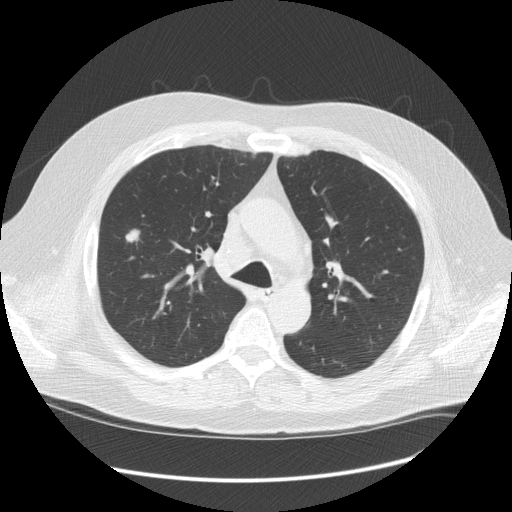
Low-dose screening chest CT, one axial slice; slice 89 of 128 in the series (ordered by position); reconstruction kernel STANDARD; lung window (W 1500 / L -600 HU); 2.5 mm slice thickness; 512 × 512 image matrix, field of view 401 × 401 mm.
Outlined on this slice (expert manual segmentation):
- lesion 1 (tumor, upper lobe of right lung): bounding box [x1, y1, x2, y2] px = [126, 230, 139, 242]